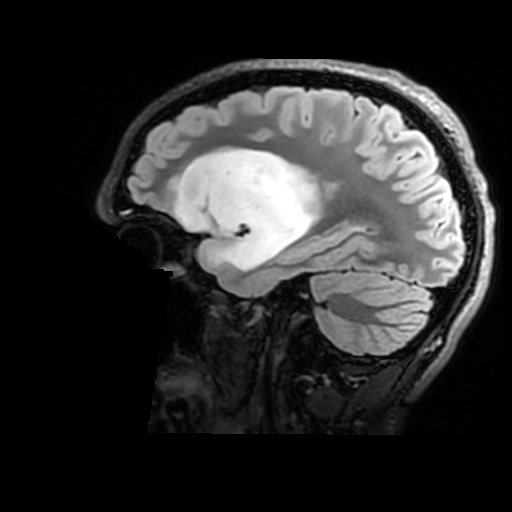
Brain MRI from a brain-tumour surgery series, one sagittal slice. Slice 118 of 176 in the series (ordered by position). T2 FLAIR. 1 mm slice thickness. 512 × 512 image matrix, field of view 240 × 240 mm. Case-level facts recorded for this patient, not image findings: histopathology: Astrocytoma; WHO grade: 2; IDH mutation: yes; tumour location: Right Insular.
Annotated regions visible in this slice (manually delineated by an expert):
- tumour: bounding box <176,147,320,273> (left, top, right, bottom; pixels)